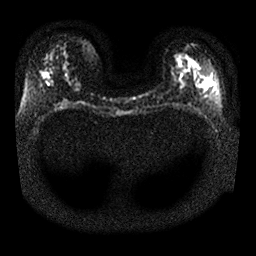
Breast MRI, one axial slice; slice 14 of 25 in the series (ordered by position); diffusion-weighted series; image 2 of 4 stored at this slice position (different b-values; order by instance number); 1.5 T; 4 mm slice thickness; 256 × 256 image matrix, field of view 340 × 340 mm. Female patient.
Annotated regions visible in this slice (outlined manually by an expert reader):
- tumour on diffusion-weighted imaging: bounding box <42,73,50,80> (left, top, right, bottom; pixels)